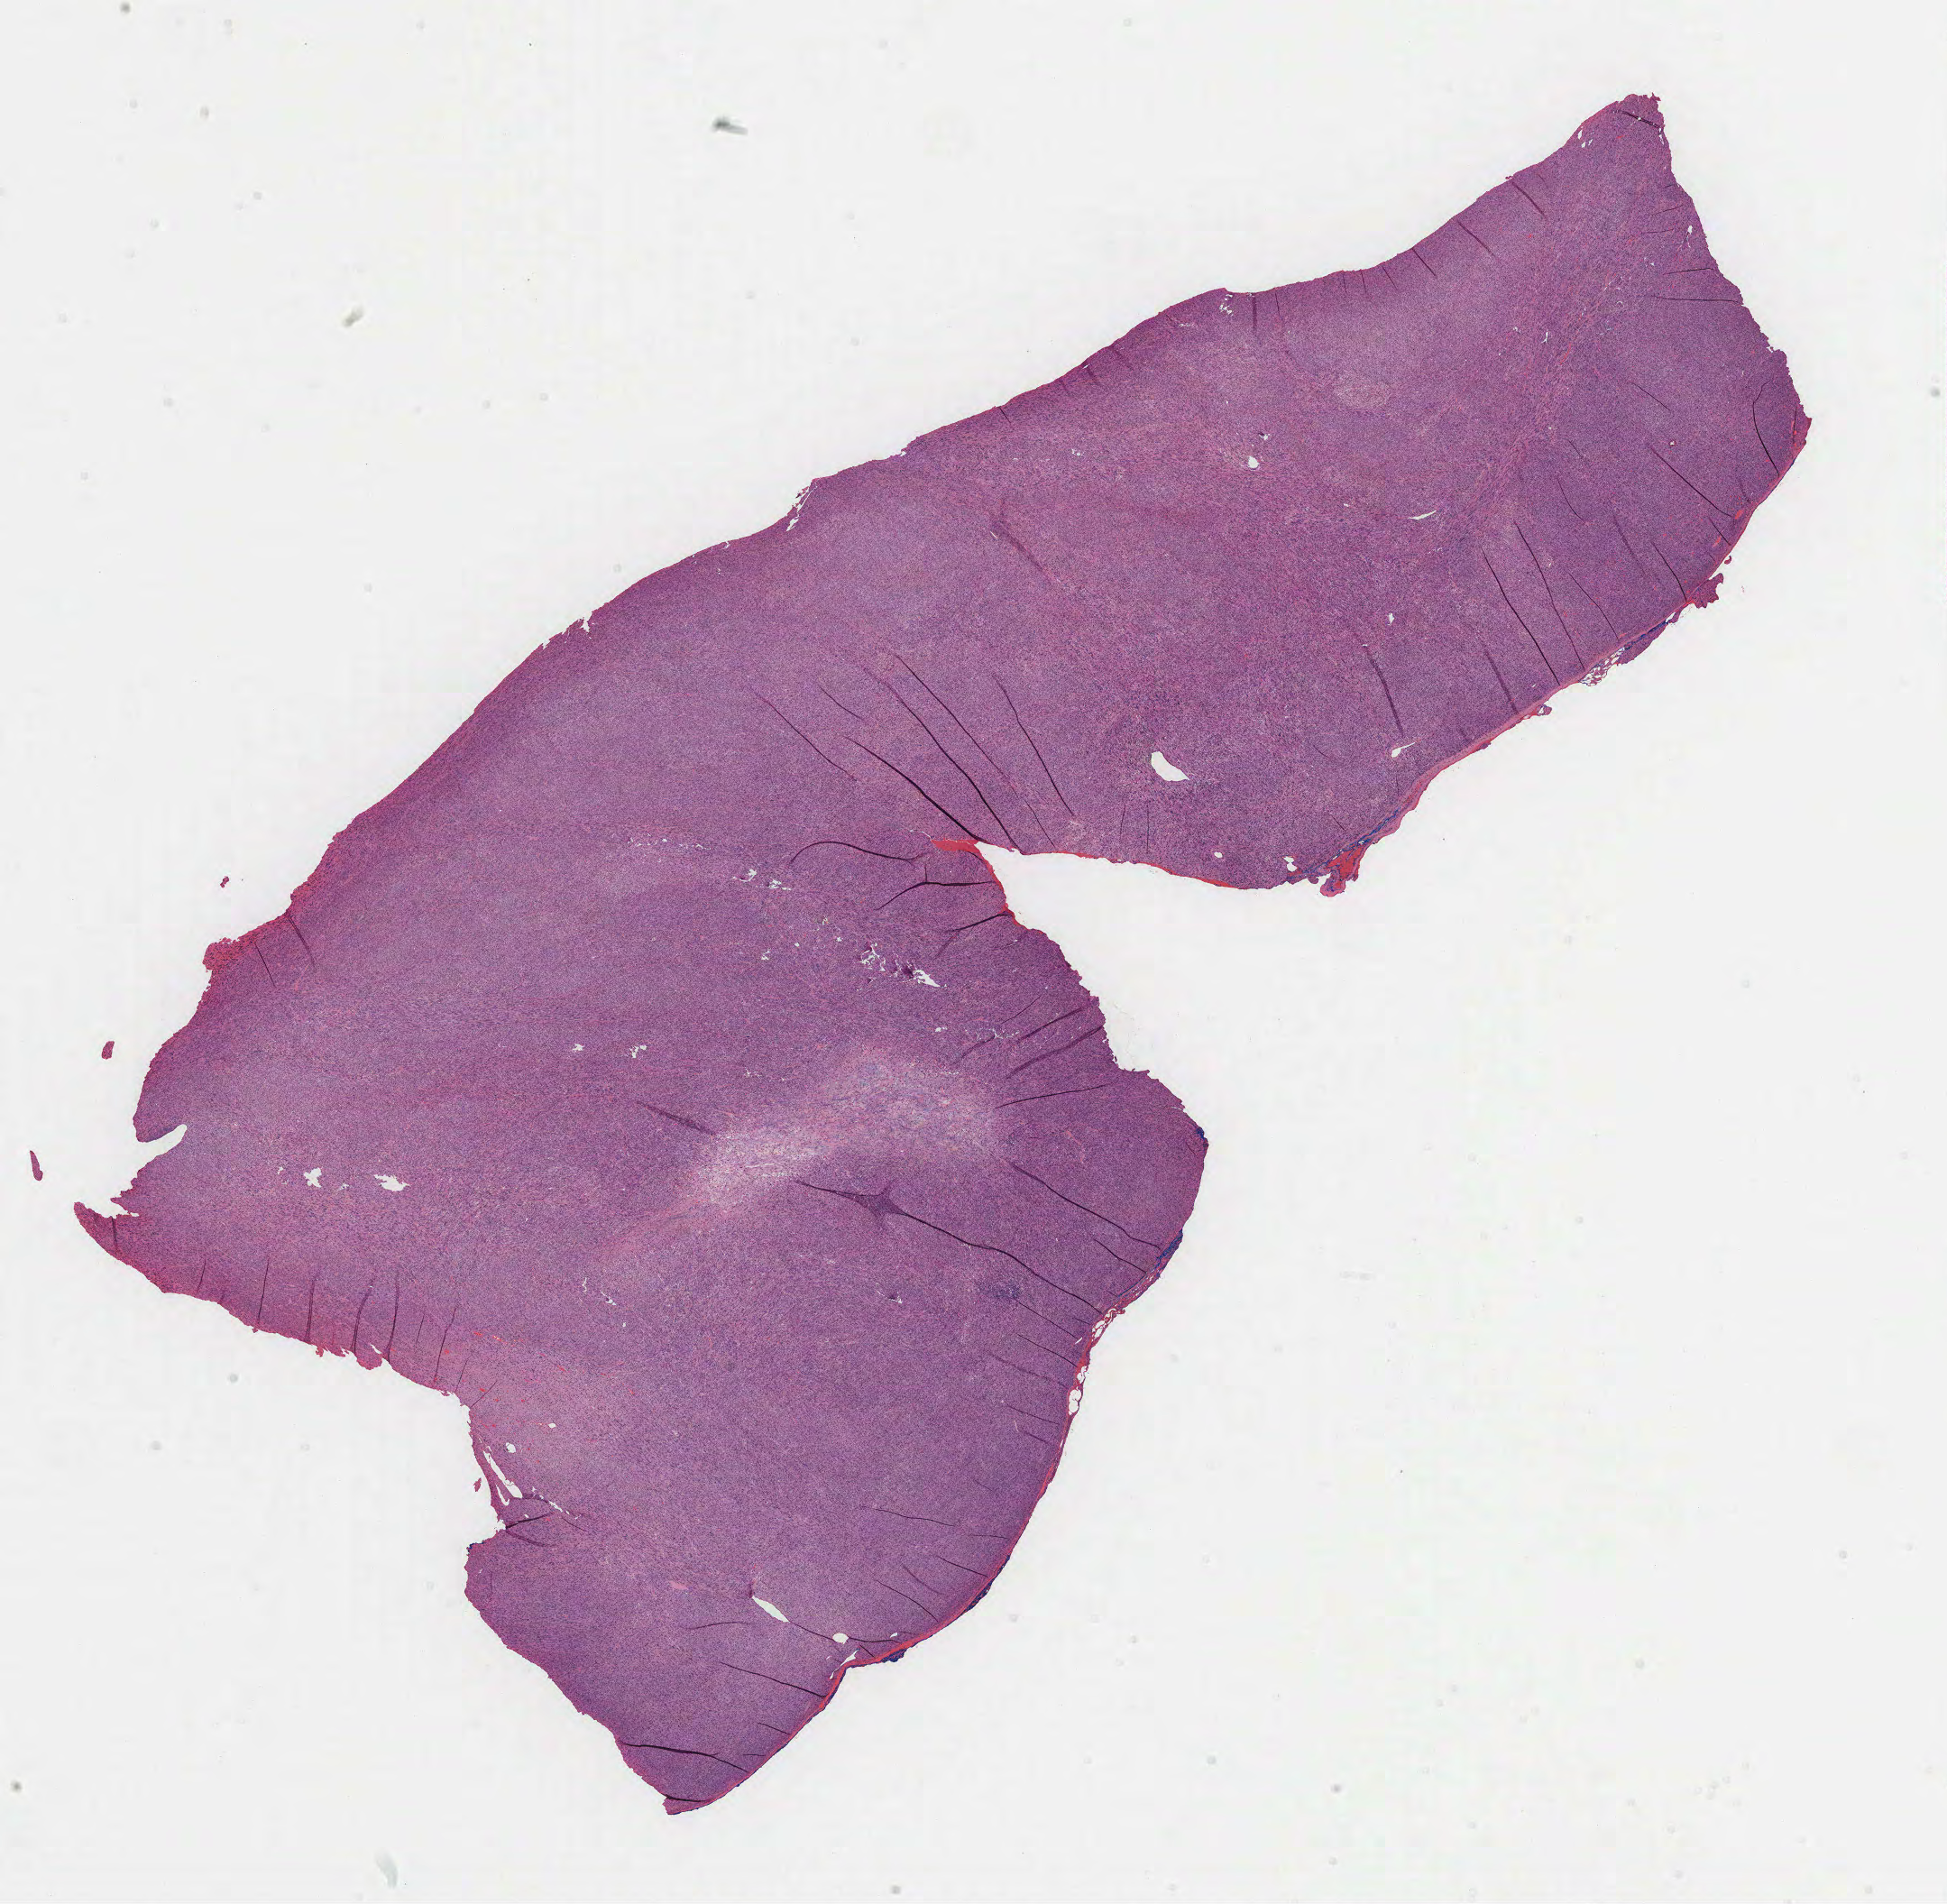
Digitized H&E tissue section (whole slide), low-resolution overview of the scanned area, about 17.4 x 17.1 mm (slide scanned at 40x), FFPE section, retroperitoneum and peritoneum, primary tumour sample. Male patient; age at initial diagnosis 33 years.
Diagnosis: Leiomyosarcoma, NOS (retroperitoneum).